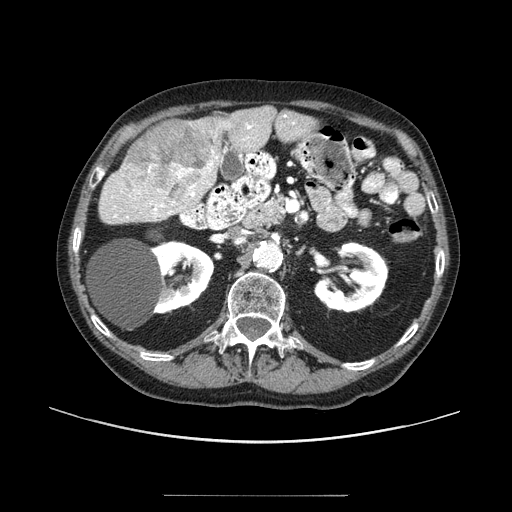
Contrast-enhanced abdominal CT (liver protocol), one axial slice. Slice 40 of 91 in the series (ordered by position). Reconstruction kernel STANDARD. 100 kVp. One of 2 acquisitions stored at this slice position. Soft-tissue window (W 400 / L 40 HU). 2.5 mm slice thickness. 512 × 512 image matrix, field of view 400 × 400 mm. Case-level facts recorded for this patient, not image findings: diagnosis: hepatocellular carcinoma (patient treated with transarterial chemoembolisation; whether this scan precedes or follows treatment is not stated here); TNM stage (as recorded): Stage-I; Child-Pugh class: A; tumour differentiation: moderately differentiated.
Annotated regions visible in this slice (semi-automatic segmentation, software-assisted and operator-edited):
- liver parenchyma outside the tumour (the mass and vessels are separate outlines, so this box may not span the whole liver): bounding box [x1, y1, x2, y2] px = [100, 106, 276, 222]
- mass: [122, 121, 216, 204]
- liver vessels: [127, 123, 252, 218]